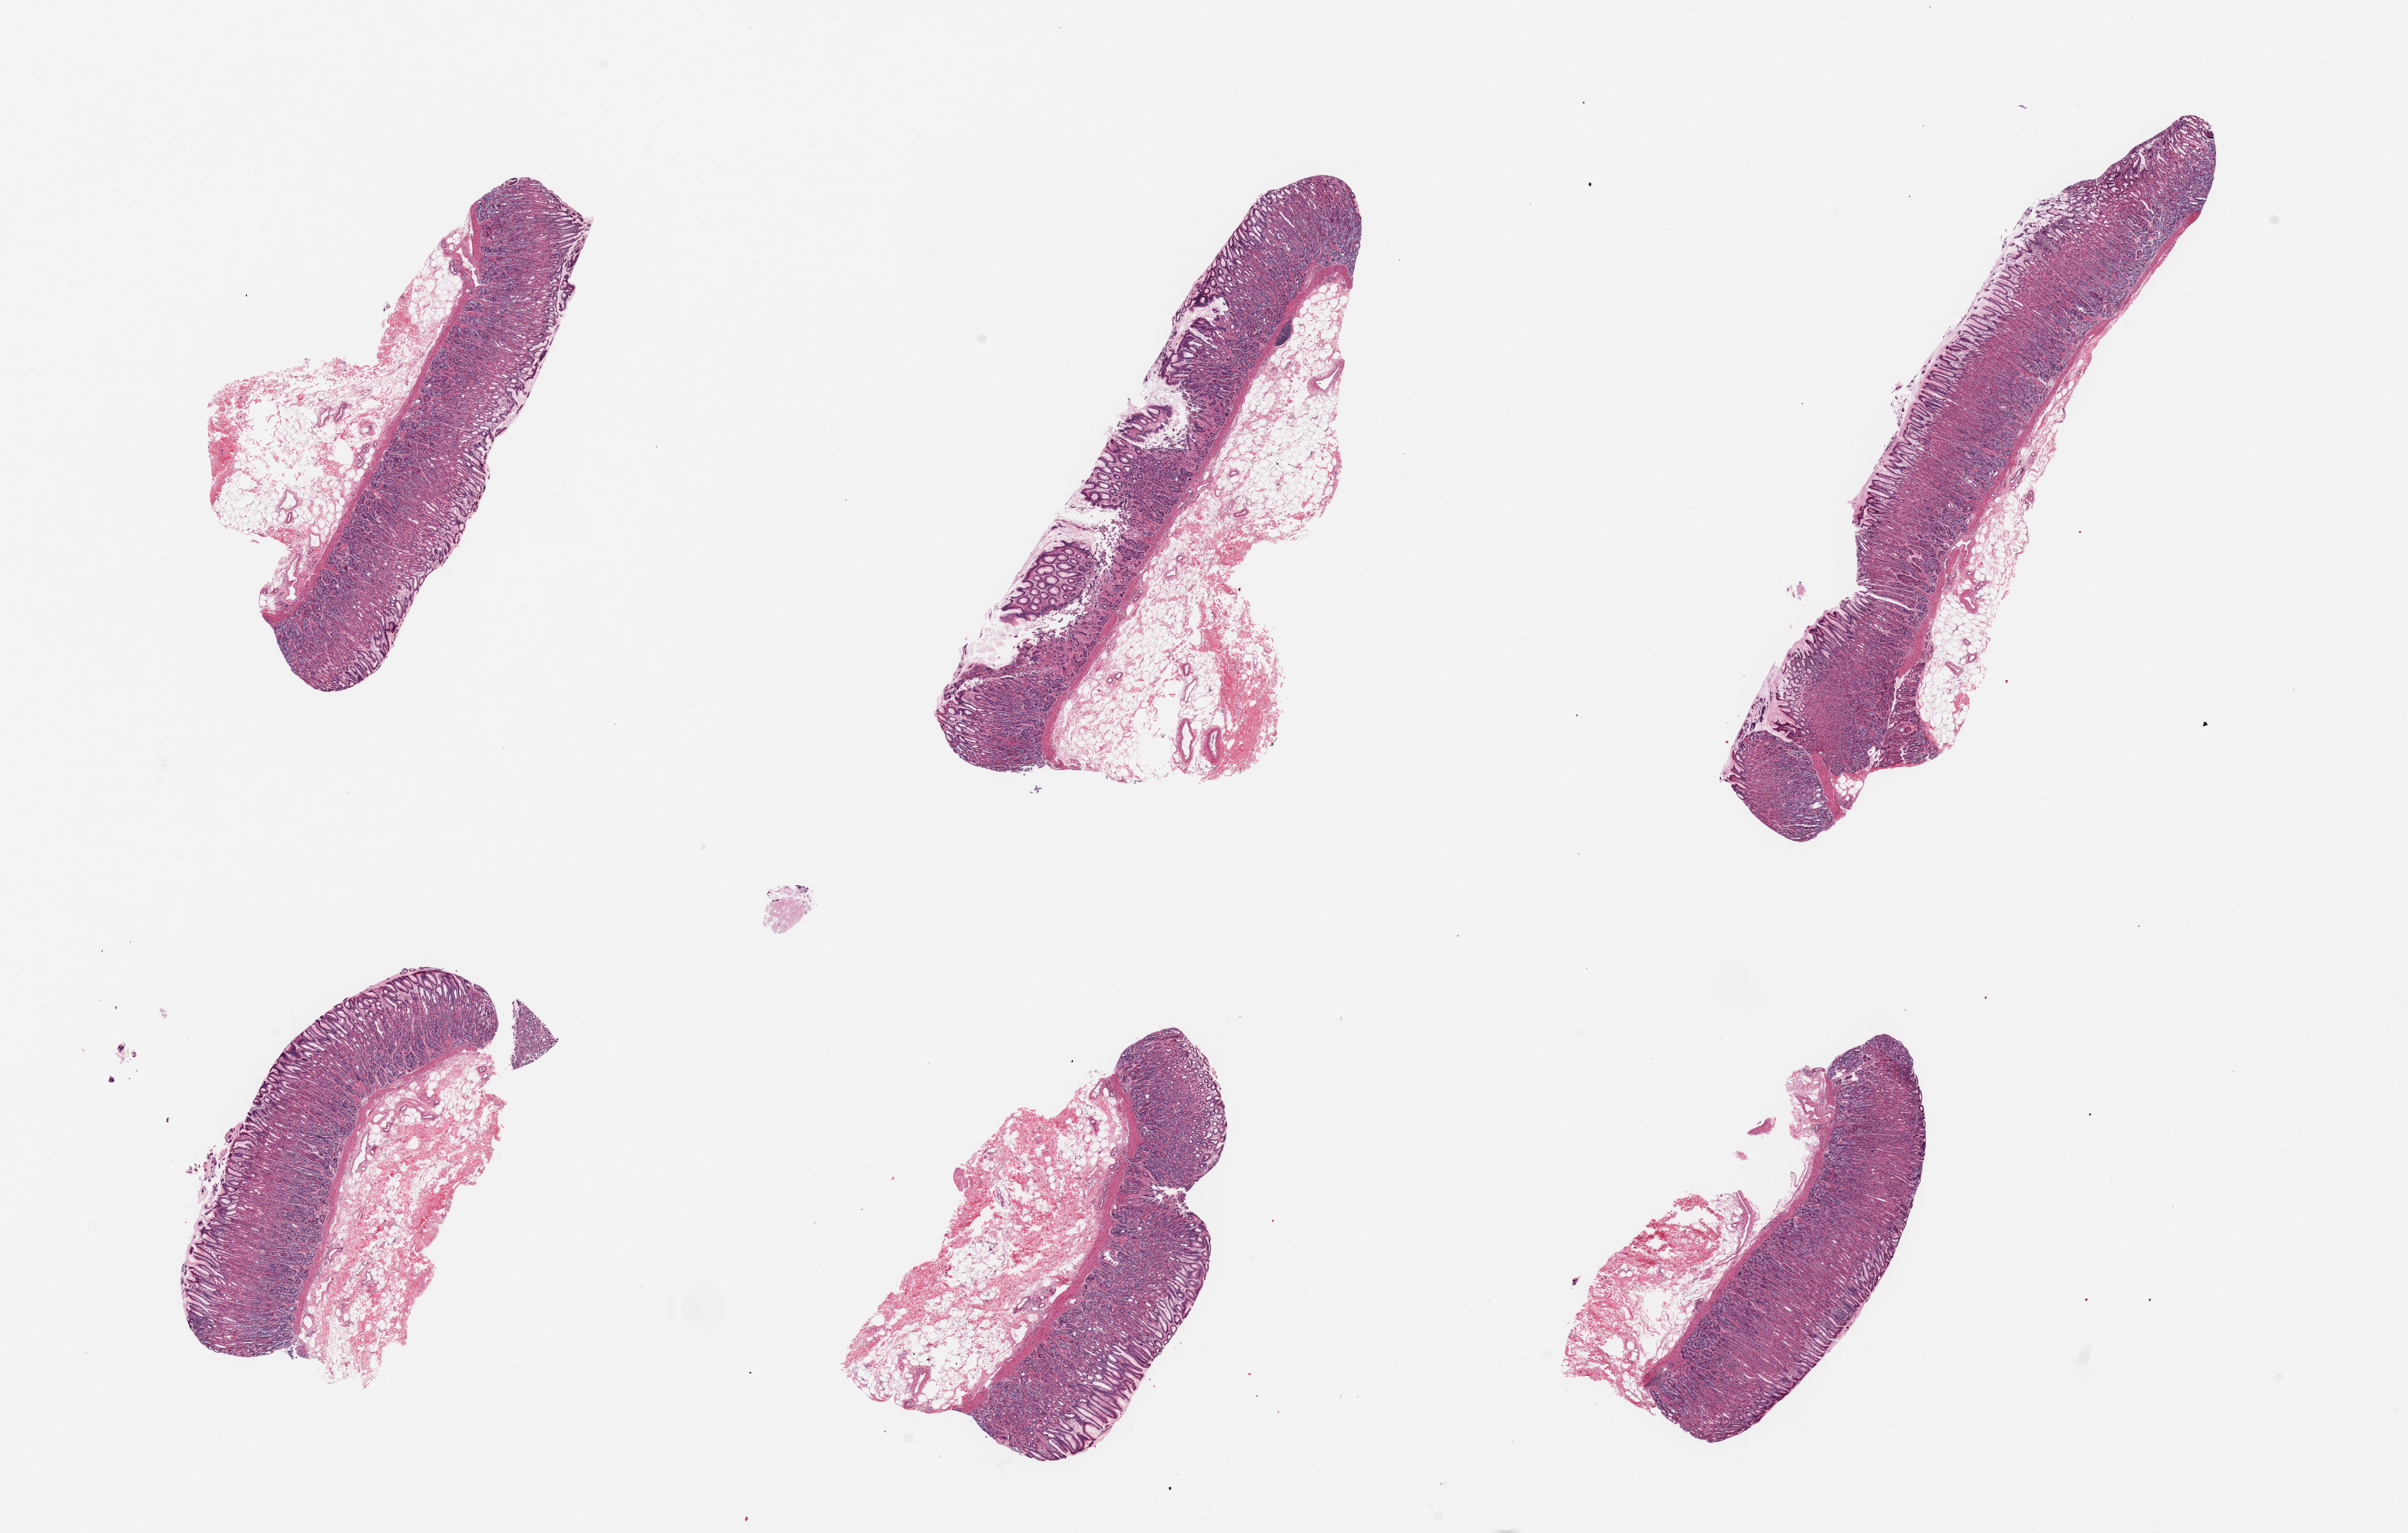
Haematoxylin and eosin whole-slide image, brightfield, a low-resolution overview of the entire scanned area, about 24.6 x 15.7 mm (slide scanned at 20x); PAXgene-fixed, paraffin-embedded tissue; target tissue: stomach; tissue donor sample.
* reviewer comment on this tissue sample: 6 pieces; well preserved mucosa and fatty submucosa; no muscularis propria